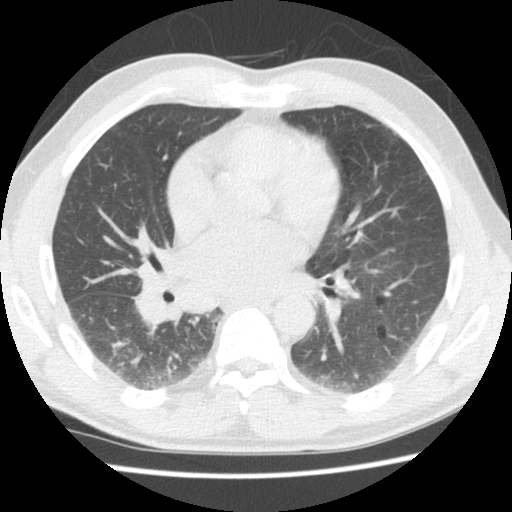
Low-dose screening chest CT, one axial slice. Reconstruction kernel STANDARD. 140 kVp. Lung window (W 1500 / L -600 HU). 512 × 512 image matrix, field of view 320 × 320 mm.
Annotated regions visible in this slice (outlined manually by an expert reader):
- lesion 1 (tumor, lower lobe of right lung): bounding box (x1, y1, x2, y2) in pixels: (112, 340, 127, 357)